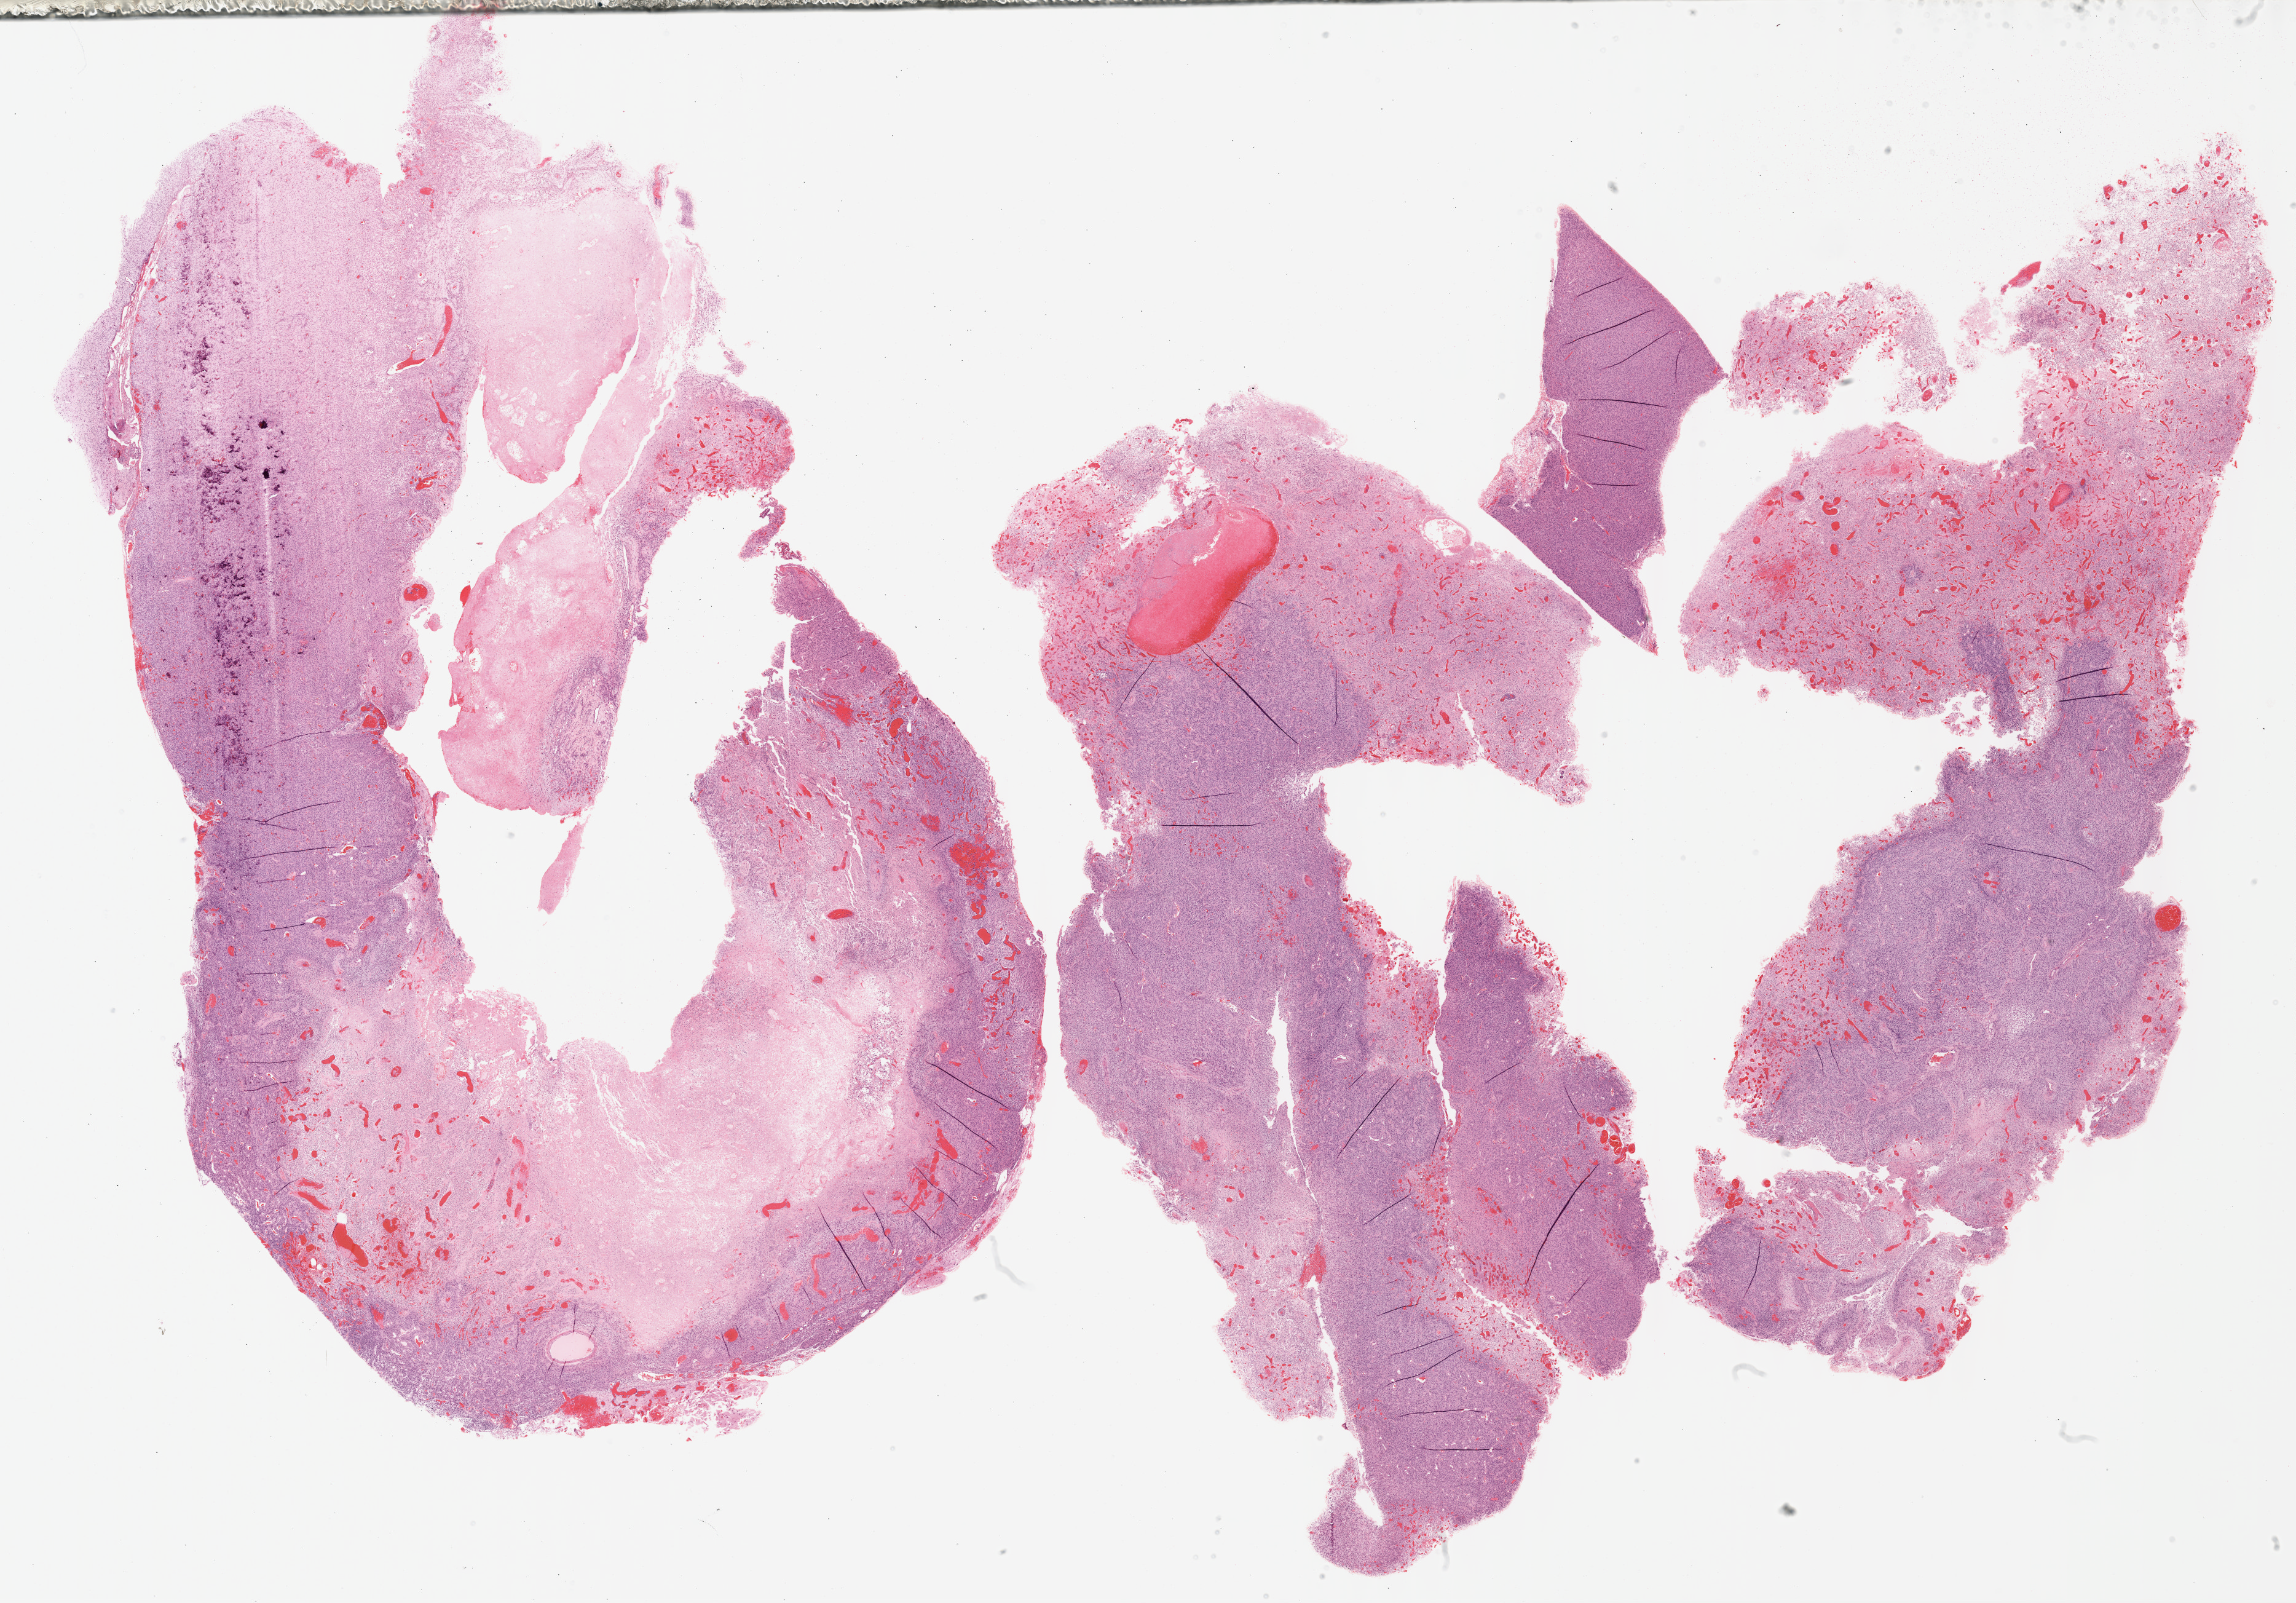
H&E whole-slide image — a low-resolution overview of the entire scanned area, about 30.2 x 21.1 mm (acquisition: 40x scan); formalin-fixed paraffin-embedded (FFPE) diagnostic section; brain, primary tumour sample. Patient: male, age at initial diagnosis 69 years.
Pathologic diagnosis: Glioblastoma.